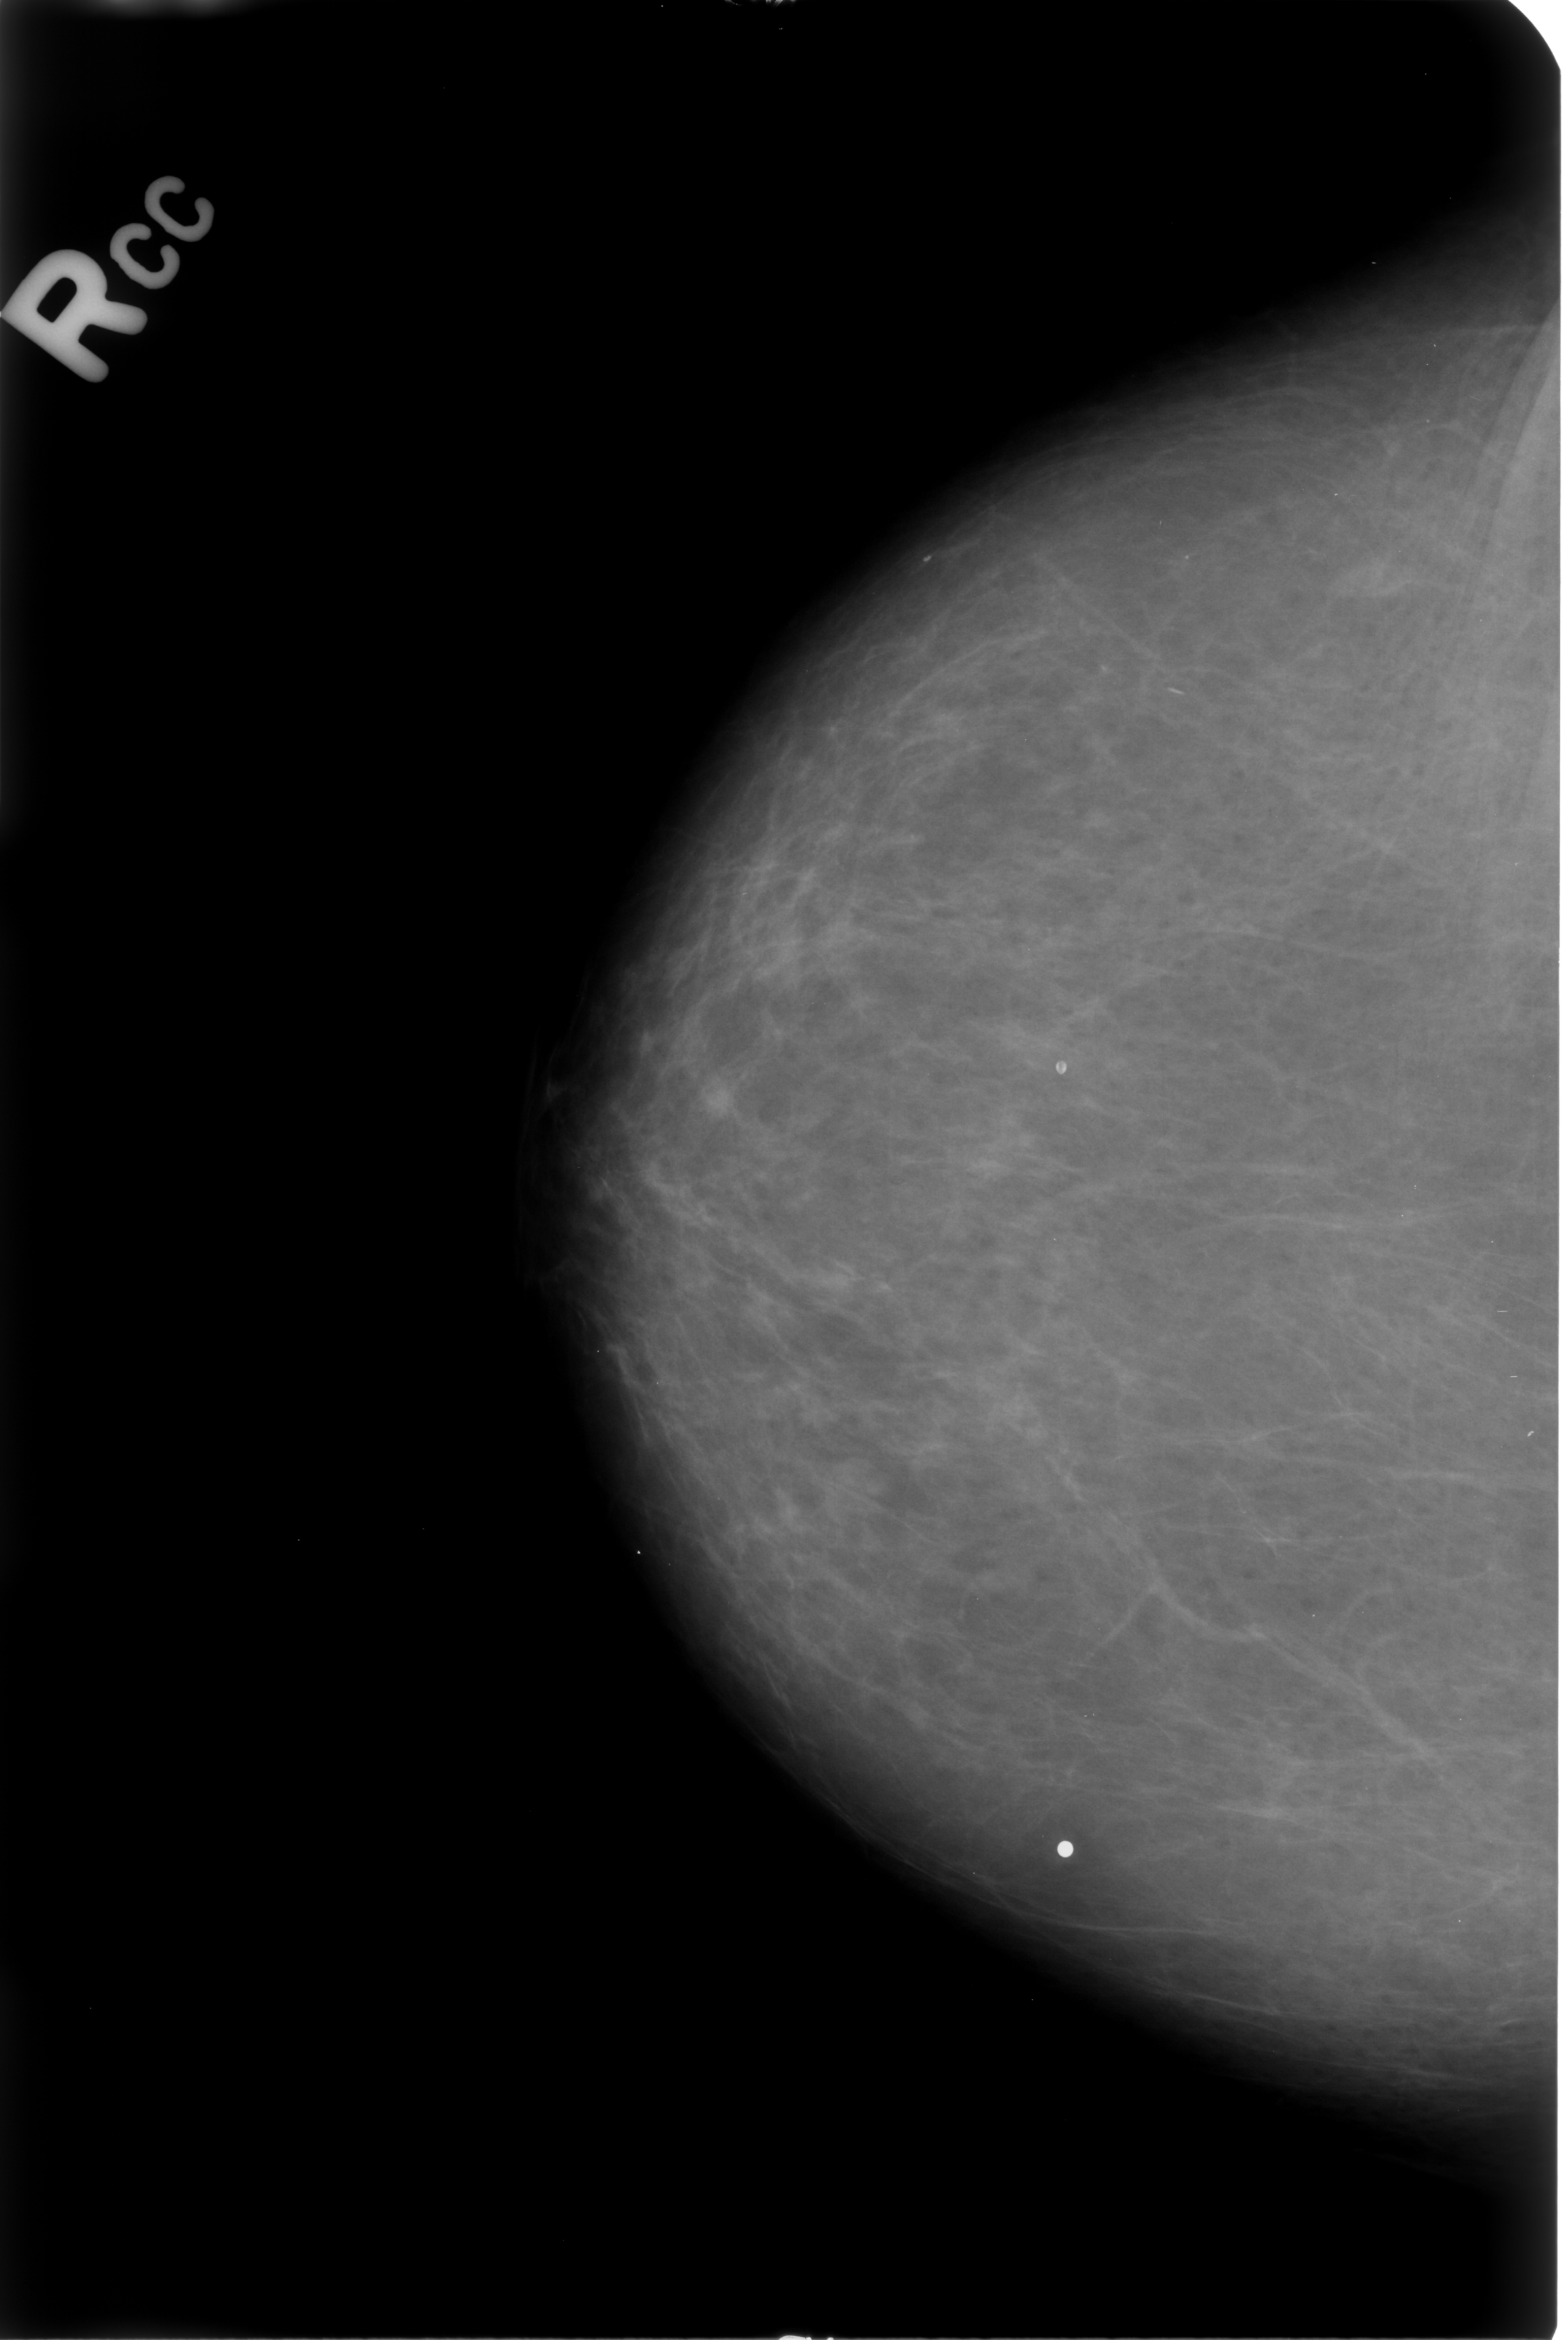
Mammogram (digitized film), right breast, CC view, breast composition: almost entirely fatty (BI-RADS density category 1 of 4).
Radiologist-marked abnormalities on this image: Finding 1 of 2: calcifications, morphology lucent center; BI-RADS assessment category 2; subtlety rating 3 on a 1 (subtle) to 5 (obvious) scale; benign without callback (not worked up further). Finding 2 of 2: calcifications, morphology lucent center; BI-RADS assessment category 2; benign; no additional work-up was recommended (benign without callback).